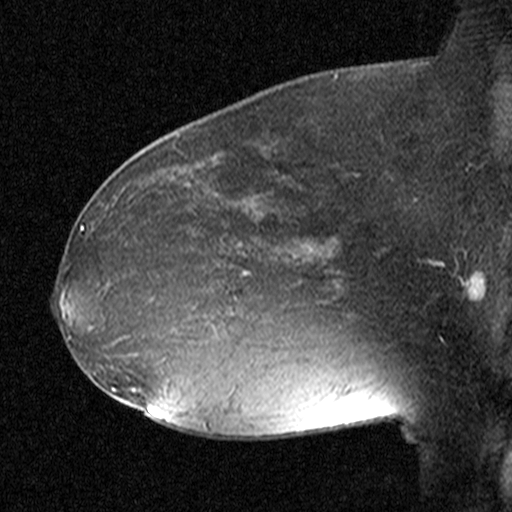
Breast MRI (dynamic contrast-enhanced), one sagittal slice; position 27 of 44 along the scan axis; dynamic contrast-enhanced study with each time point stored as its own series, time point 2 of 3 at this slice position (early post-contrast, ordered by acquisition time); 1.5 T; TE 4.5 ms, TR 11 ms; 3 mm slice thickness; 512 × 512 image matrix, field of view 200 × 200 mm. Patient: female, 38 years. From the clinical record (not read from this slice): setting: breast cancer imaged before/during neoadjuvant chemotherapy; receptor status: HR-positive, HER2-negative.
Annotated regions visible in this slice (semi-automatically segmented with operator editing):
- analysis volume of interest (the breast-tissue region the enhancement analysis was run in; not a lesion): bounding box (x1, y1, x2, y2) in pixels: (182, 232, 291, 349)
- tumour enhancement mask (voxels above the 90 % enhancement threshold inside the analysis volume of interest): (243, 236, 251, 273)